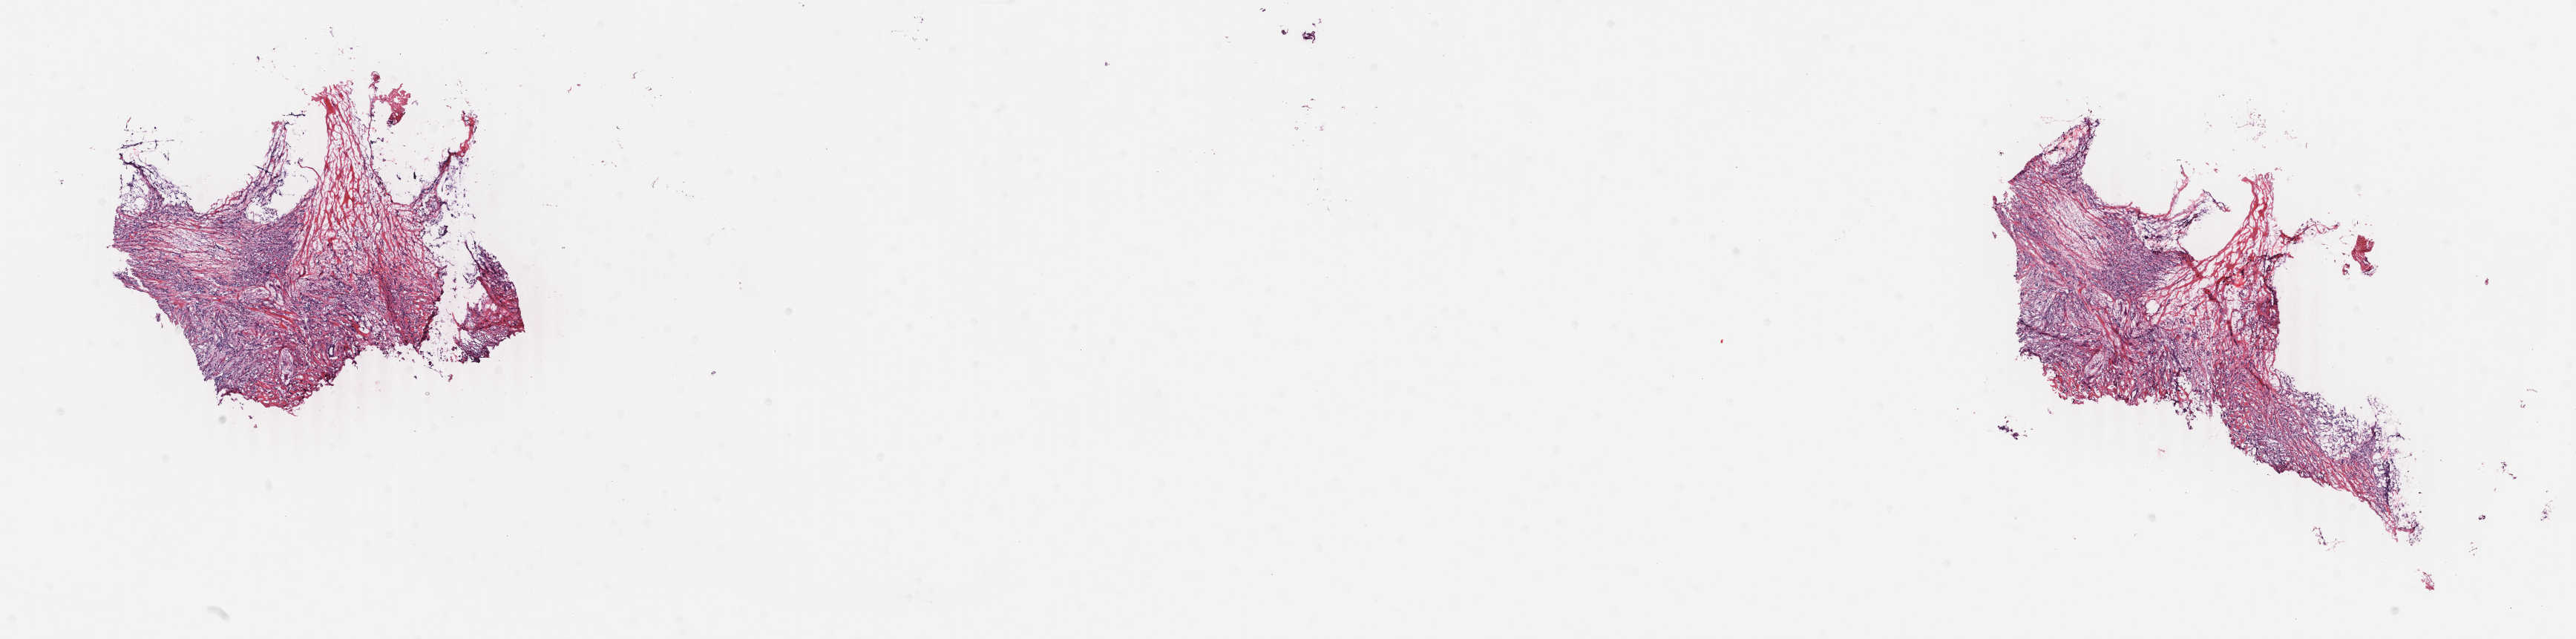
H&E whole-slide image — low-resolution overview of the scanned area, about 27.6 x 6.8 mm (acquisition: 40x scan). Frozen section. Sample: primary tumour, breast. Female, age 50 years at initial diagnosis. Pathologist review of this section (percent, as recorded): tumour cells 80%, tumour nuclei 80%, normal cells 0%, stromal cells 15%, necrosis 5%. Inflammatory infiltration, as recorded: lymphocyte infiltration 40%, monocyte infiltration 10%, neutrophil infiltration 10%.
AJCC pathologic stage: IIB. Lymph nodes positive (case pathology): 0 of 3 examined. Pathologic diagnosis: Lobular carcinoma, NOS.